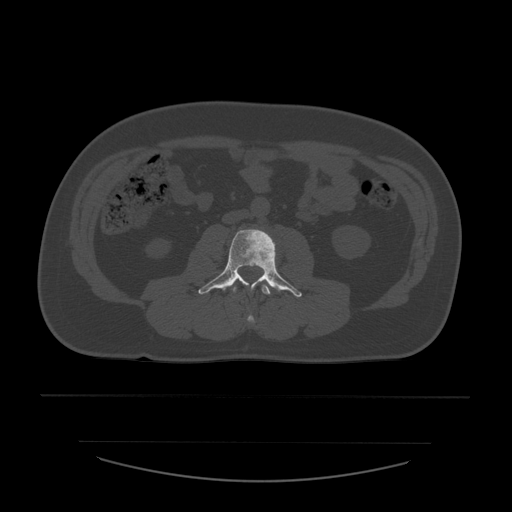
CT including the spine, one axial slice; slice 178 of 532 in the series (ordered by position); reconstruction kernel STANDARD; 120 kVp; bone window (W 1800 / L 400 HU); 1.25 mm slice thickness; 512 × 512 image matrix, field of view 441 × 441 mm. Patient age 44 years. From the clinical record (not read from this slice): primary cancer: soft tissue sarcoma.
Outlined on this slice (semi-automatic segmentation, software-assisted and operator-edited):
- L2 vertebra: bounding box <233,285,271,323> (left, top, right, bottom; pixels)
- L3 vertebra: <199,229,302,297>